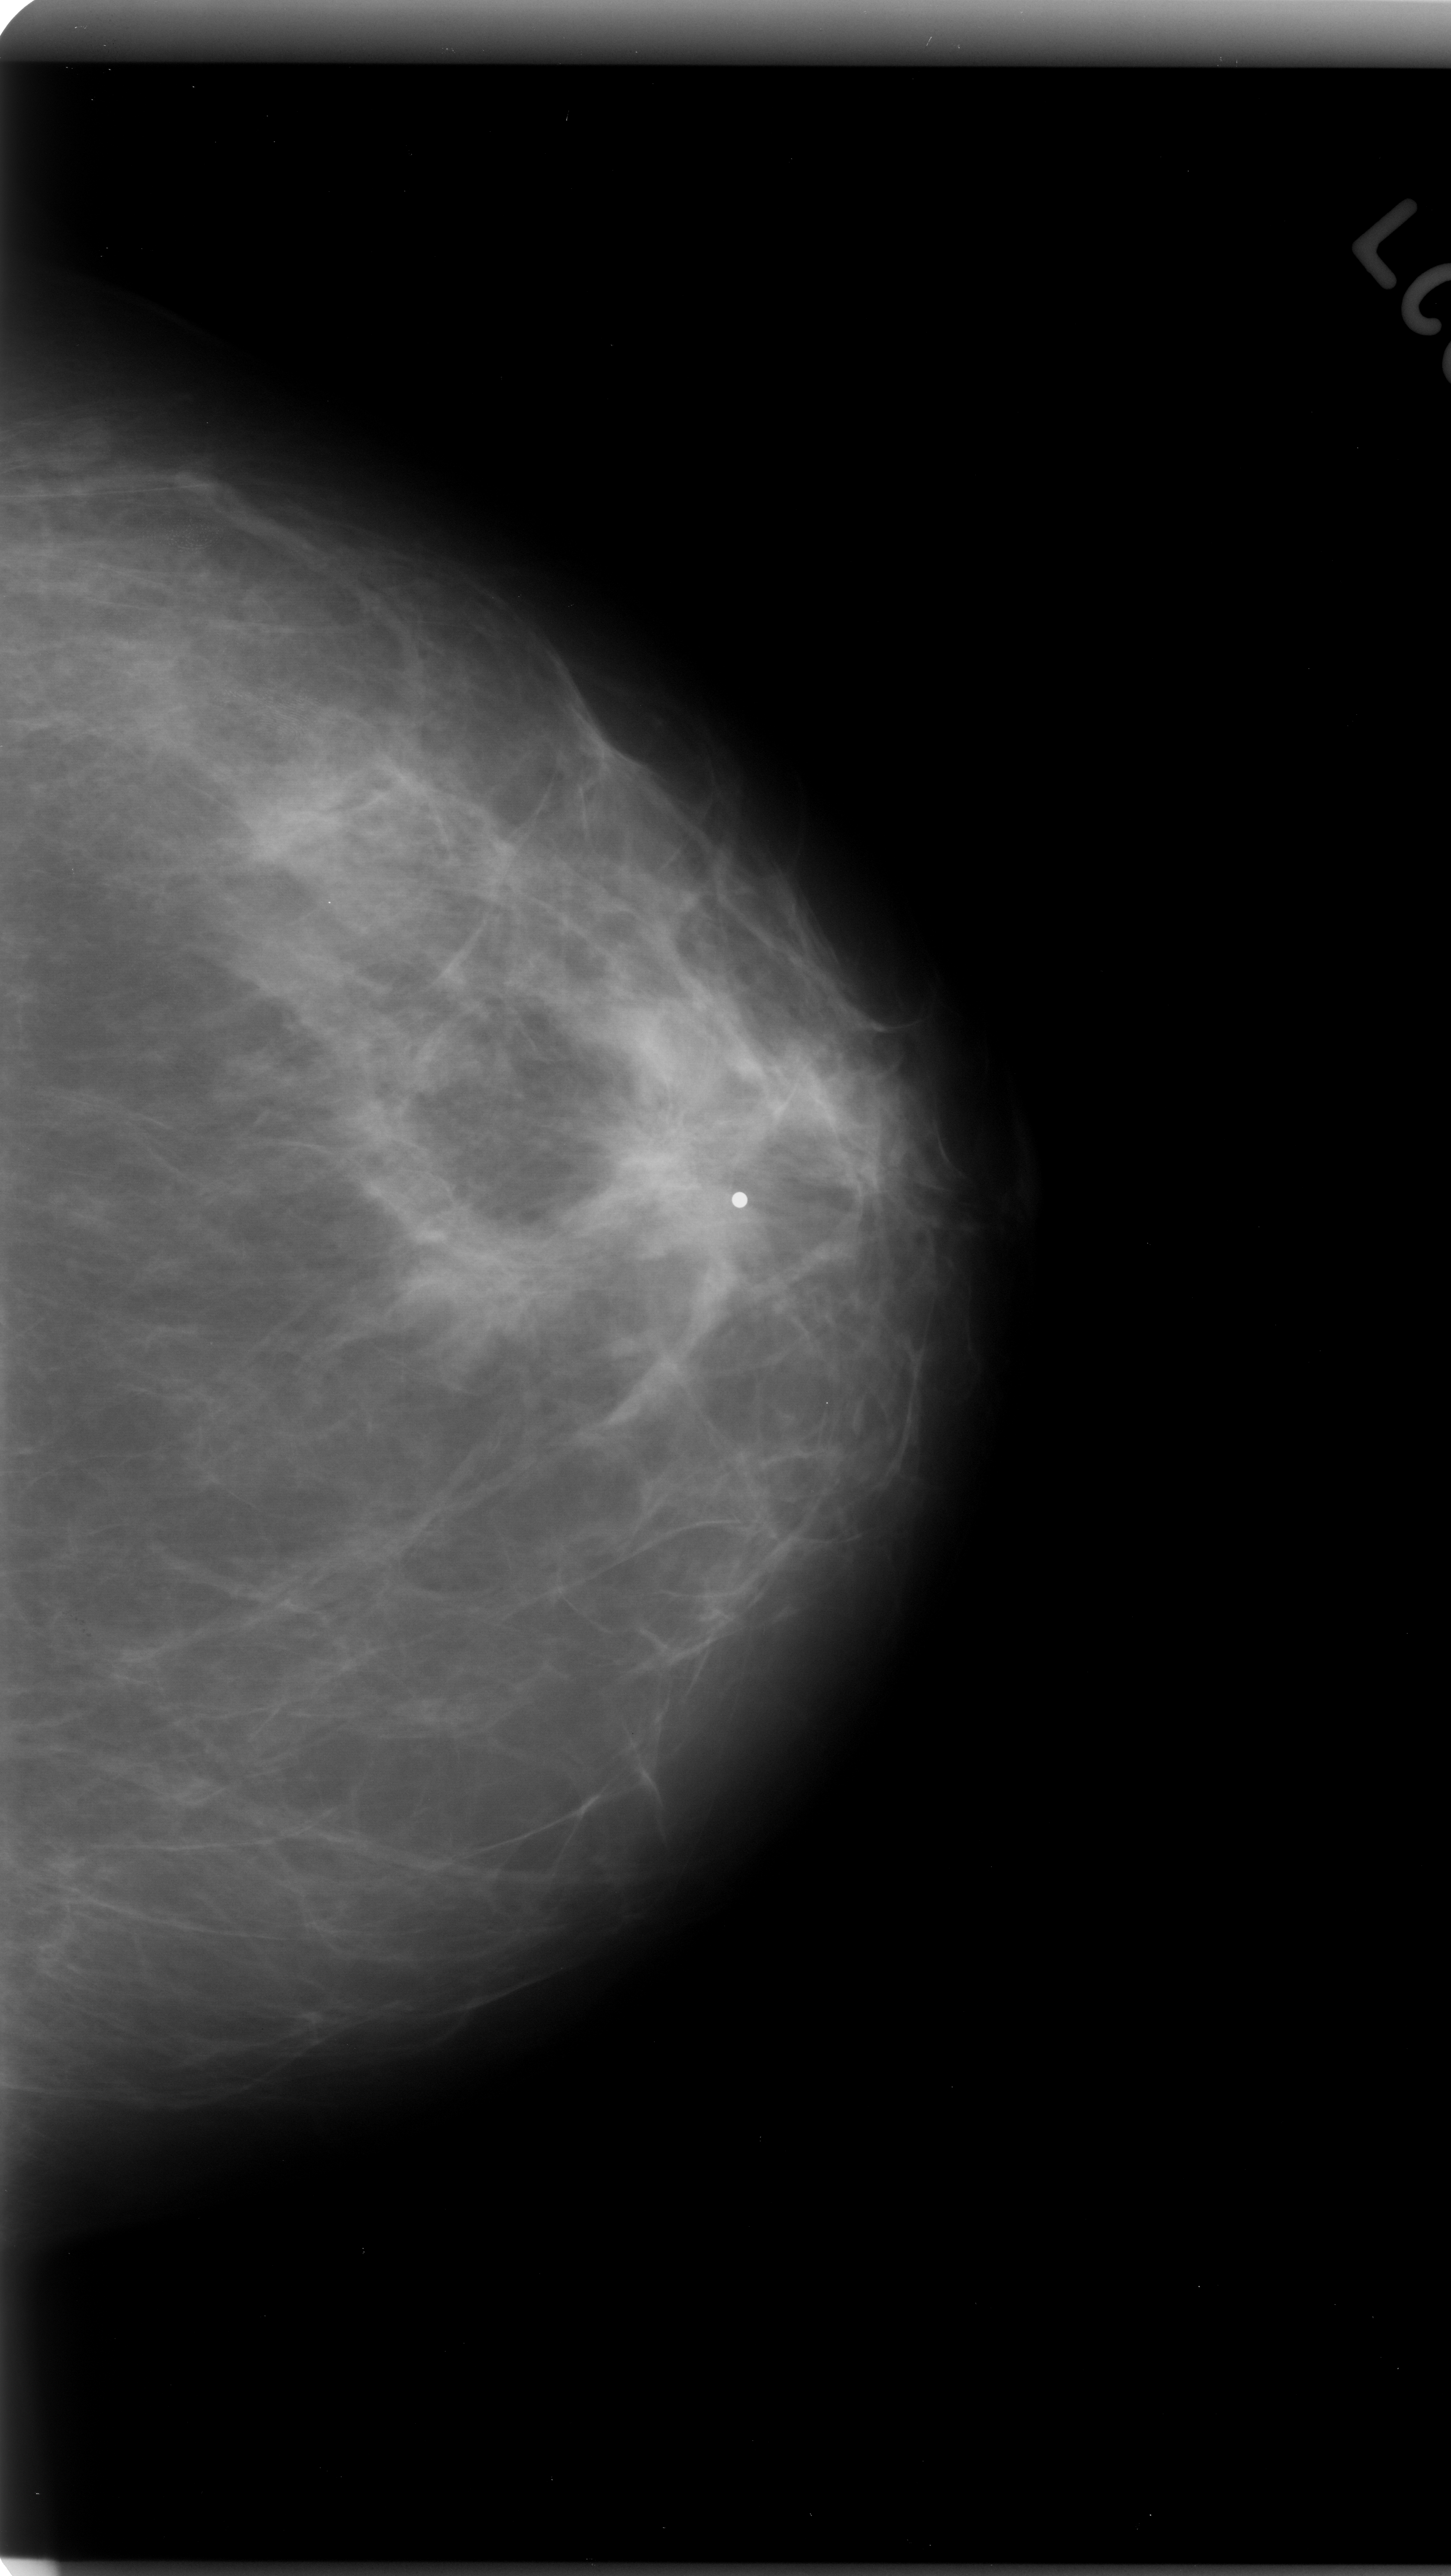
Scanned film-screen mammogram, left breast, CC view, breast composition: scattered fibroglandular densities (BI-RADS density category 2 of 4).
Finding: mass, shape architectural distortion, margins spiculated; BI-RADS assessment category 5; pathology (as recorded): malignant.